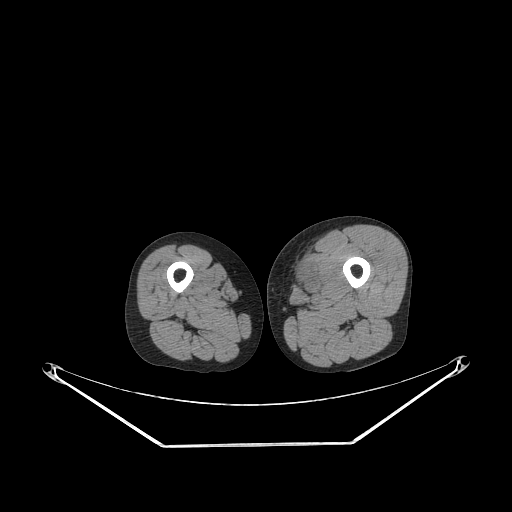
CT of an extremity soft-tissue mass (from a PET/CT study), one axial slice; slice 229 of 267 in the series (ordered by position); reconstruction kernel STANDARD; 140 kVp; soft-tissue window (W 400 / L 40 HU); 3.75 mm slice thickness; 512 × 512 image matrix. Male patient. Case-level facts recorded for this patient, not image findings: histological type: pleiomorphic leiomyosarcoma; grade: high; site of the primary tumour: left thigh.
Structures marked on this image (expert contour drawn on MRI and transferred to this co-registered scan by the dataset authors):
- gross tumour volume including surrounding oedema: bounding box [x1, y1, x2, y2] px = [290, 256, 316, 291]
- gross tumour volume (mass): [295, 267, 312, 291]